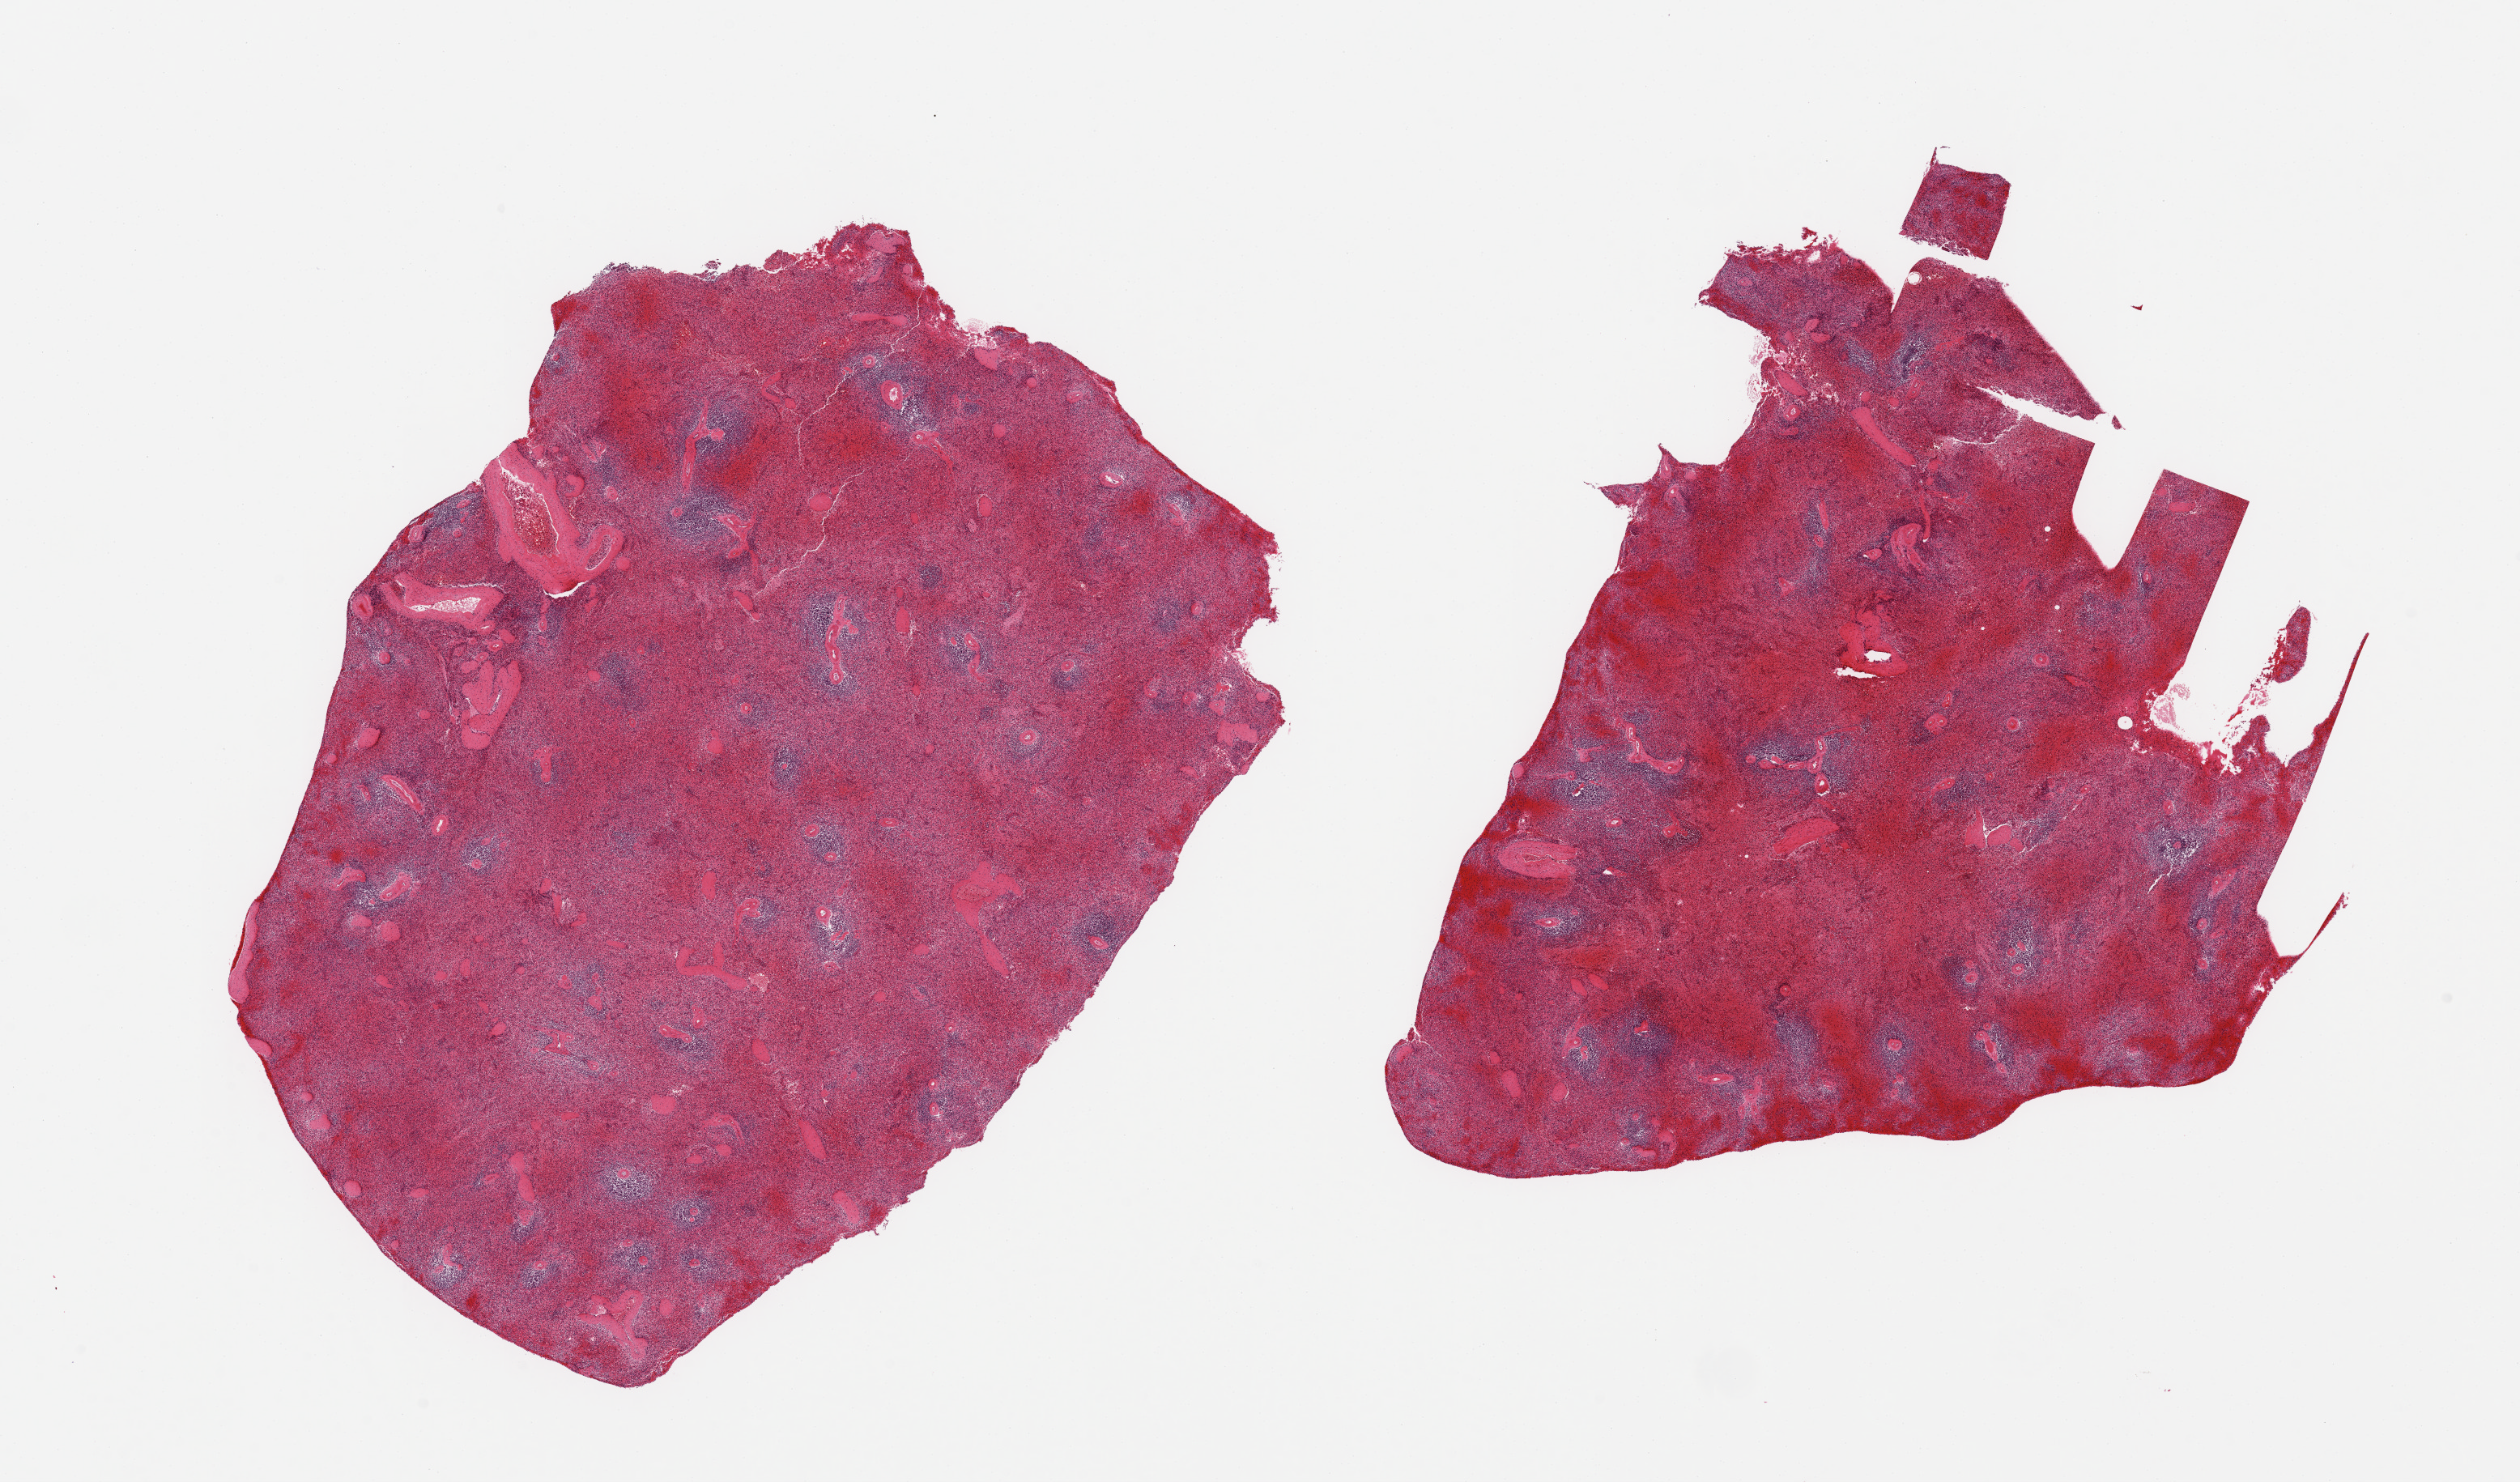
Whole-slide image, H&E stain — a low-resolution overview of the entire scanned area, about 24.6 x 14.5 mm, PAXgene-fixed paraffin-embedded (PFPE) section, sampled site (target tissue): spleen, tissue donor sample. Donor: male.
Pathologist's review note for this sample: 2 pieces; congestion.